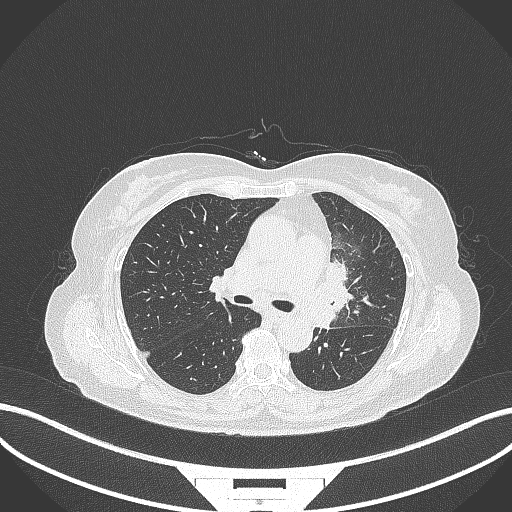
Chest CT, one axial slice; position 203 of 382 along the scan axis; 120 kVp; lung window (W 1500 / L -600 HU); 1 mm slice thickness; 512 × 512 image matrix, field of view 400 × 400 mm. Patient: female, 64 years. From the clinical record (not read from this slice): clinical TNM (as recorded): T2a N2 M0.
Structures marked on this image (rectangle marked by the reading radiologist):
- lung tumour (recorded histology: adenocarcinoma): bounding box (x1, y1, x2, y2) in pixels: (319, 254, 356, 335)